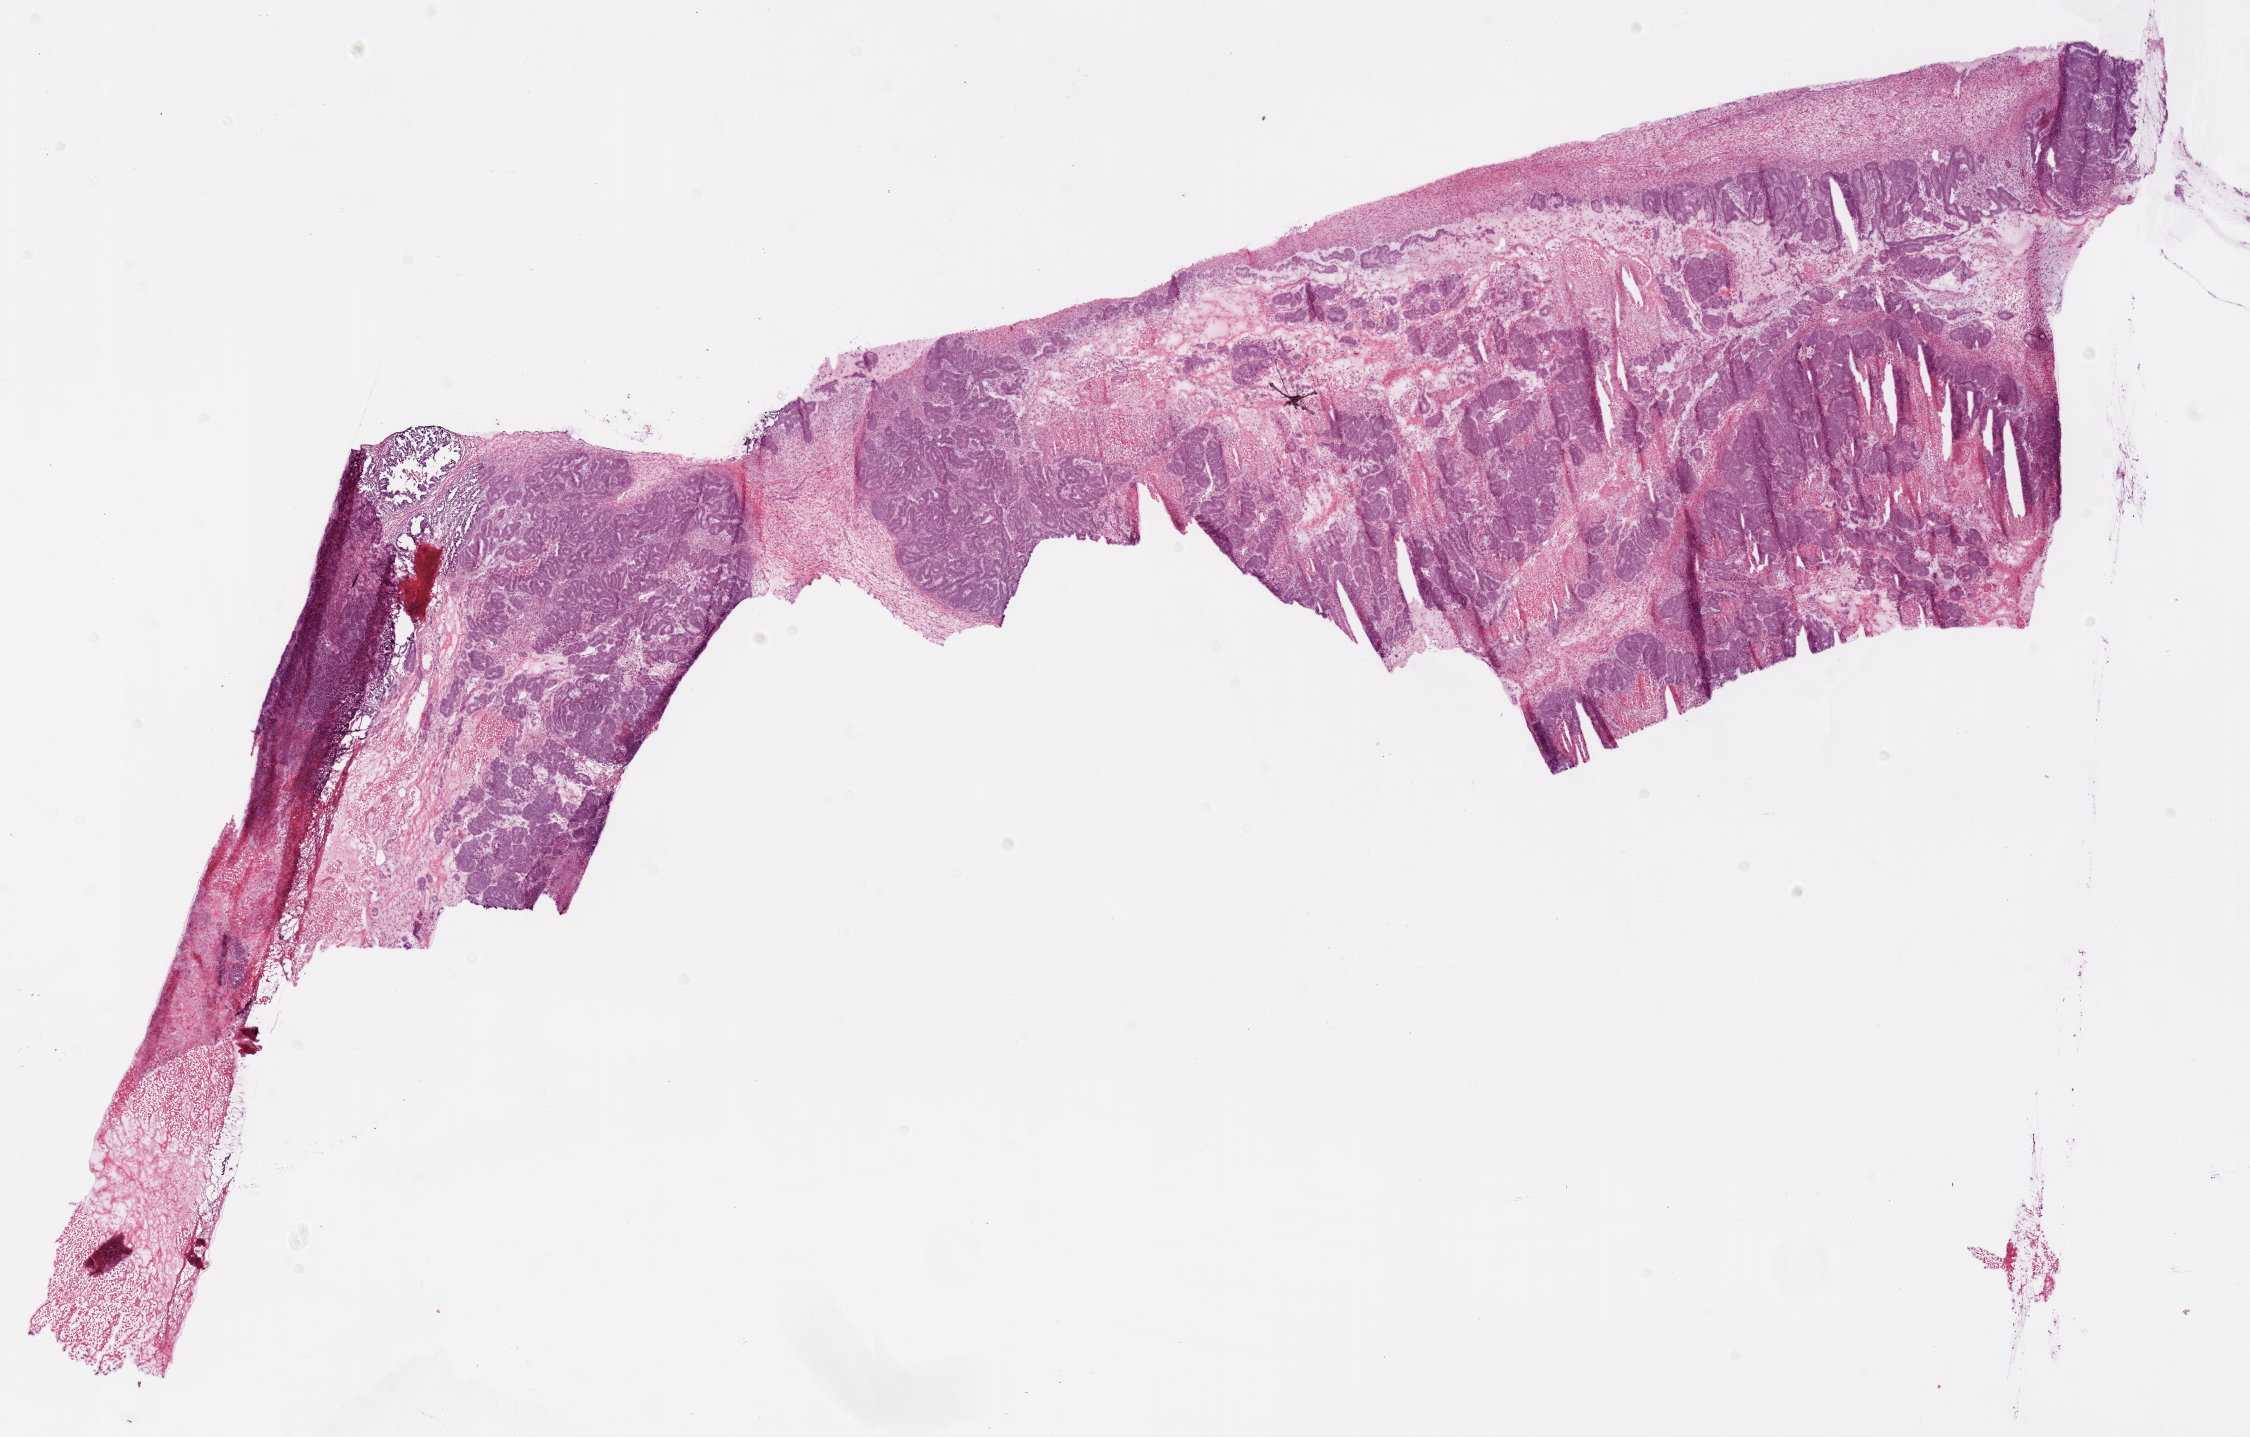
Hematoxylin and eosin (H&E) stained whole-slide image, whole scanned area (about 18.1 x 11.5 mm, slide scanned at 20x) shown as a low-resolution overview. Frozen section from the bottom of the tissue portion. Sample: primary tumour, ovary. Patient: female, age at initial diagnosis 43 years. Histologic grade: G2 (moderately differentiated). Pathologist review of this section (percent, as recorded): tumour cells 50%, tumour nuclei 70%, normal cells 0%, stromal cells 40%, necrosis 10%.
FIGO stage: IIC. Pathologic diagnosis: Serous cystadenocarcinoma, NOS. Laterality: bilateral.